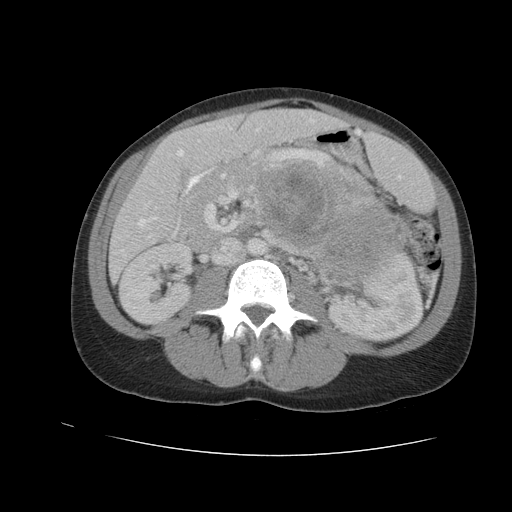
Contrast-enhanced abdominal CT, one axial slice; position 52 of 90 along the scan axis; reconstruction kernel STANDARD; intravenous contrast given; soft-tissue window (W 400 / L 40 HU); 512 × 512 image matrix. Female patient. From the clinical record (not read from this slice): diagnosis: adrenocortical carcinoma; tumour side: left adrenal.
Annotated regions visible in this slice (semi-automatic segmentation, software-assisted and operator-edited):
- mass: box from (x=259, y=162) to (x=405, y=283) px